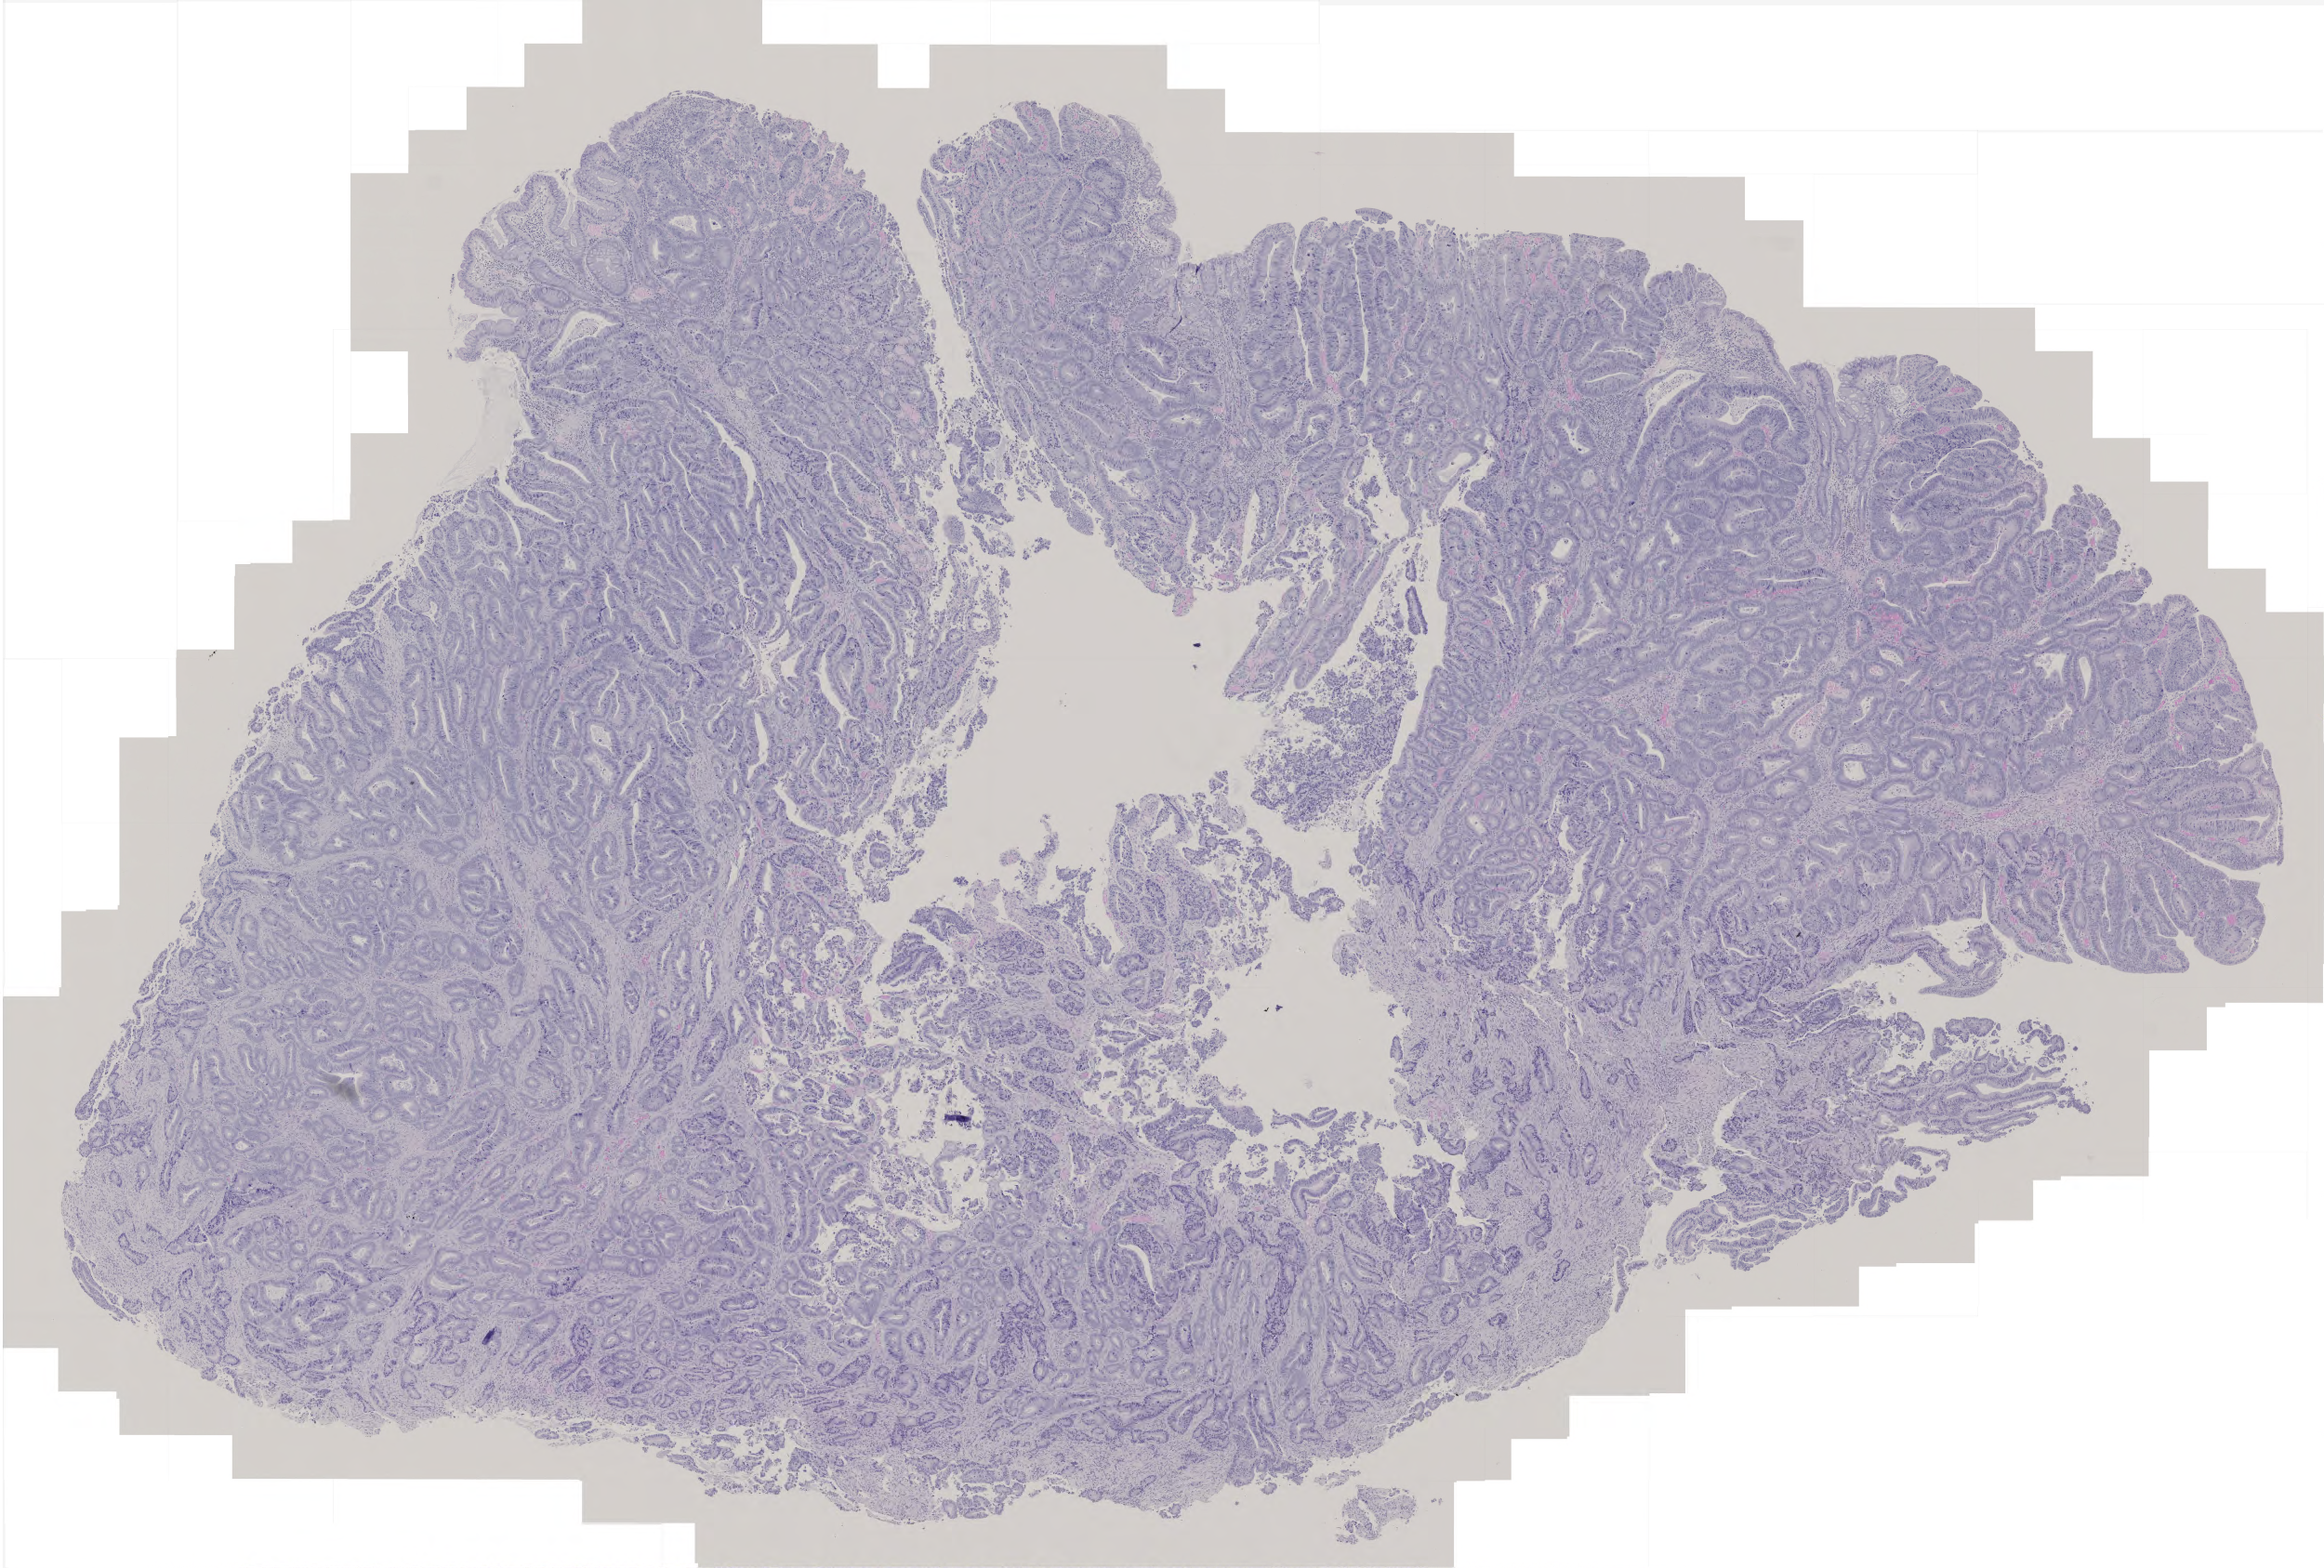
H&E-stained whole-slide image, low-resolution overview of the scanned area, about 5.0 x 3.4 mm, FFPE section, primary tumour sample from the rectum. Male patient; age at initial diagnosis 68 years.
Diagnosis: Adenocarcinoma, NOS.